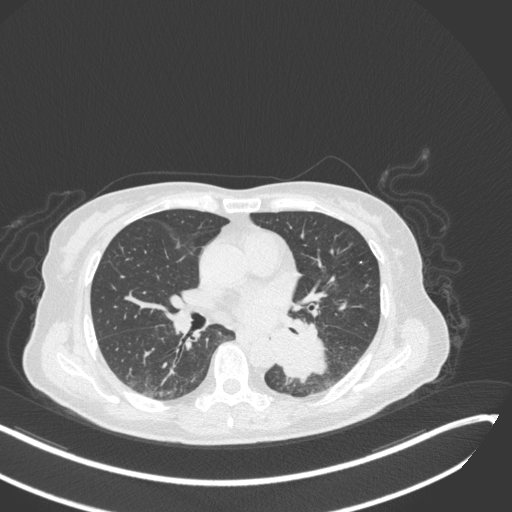
Chest CT, one axial slice. Slice 140 of 342 in the series (ordered by position). 120 kVp. Lung window (W 1500 / L -600 HU). 1 mm slice thickness. 512 × 512 image matrix. Patient: female, 64 years. From the clinical record (not read from this slice): clinical TNM (as recorded): T3 N1 M1; histopathological grade: G3.
Outlined on this slice (bounding box drawn by a radiologist):
- lung tumour (recorded histology: small cell carcinoma): bounding box <273,328,331,384> (left, top, right, bottom; pixels)